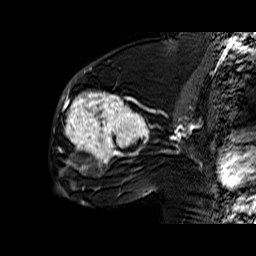
Breast MRI (dynamic contrast-enhanced), one sagittal slice. Slice 32 of 60 in the series (ordered by position). Dynamic contrast-enhanced series, time point 2 of 6 at this slice position (early post-contrast). 1.5 T. TE 6.4 ms, TR 32.9 ms. 4 mm slice thickness. 256 × 256 image matrix, field of view 200 × 200 mm. Female patient. From the clinical record (not read from this slice): setting: breast cancer imaged before/during neoadjuvant chemotherapy; receptor status: triple-negative.
Structures marked on this image (semi-automatically segmented with operator editing):
- analysis volume of interest (the breast-tissue region the enhancement analysis was run in; not a lesion): bounding box <55,65,159,174> (left, top, right, bottom; pixels)
- tumour enhancement mask (voxels above the 100 % enhancement threshold inside the analysis volume of interest): <58,71,149,174>